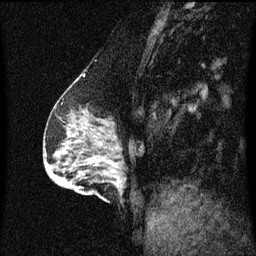
Breast MRI (dynamic contrast-enhanced), one sagittal slice. Dynamic contrast-enhanced series, image 2 of 3 at this slice position (ordered by acquisition). 1.5 T. TE 4.2 ms, TR 8.4 ms. 256 × 256 image matrix, field of view 200 × 200 mm. Female patient, age 64 years.
Annotated regions visible in this slice (semi-automatically segmented with operator editing):
- analysis volume of interest (the breast-tissue region the enhancement analysis was run in; not a lesion): bounding box <90,164,127,203> (left, top, right, bottom; pixels)
- tumour enhancement mask (voxels above the 70 % enhancement threshold inside the analysis volume of interest): <112,166,119,173>